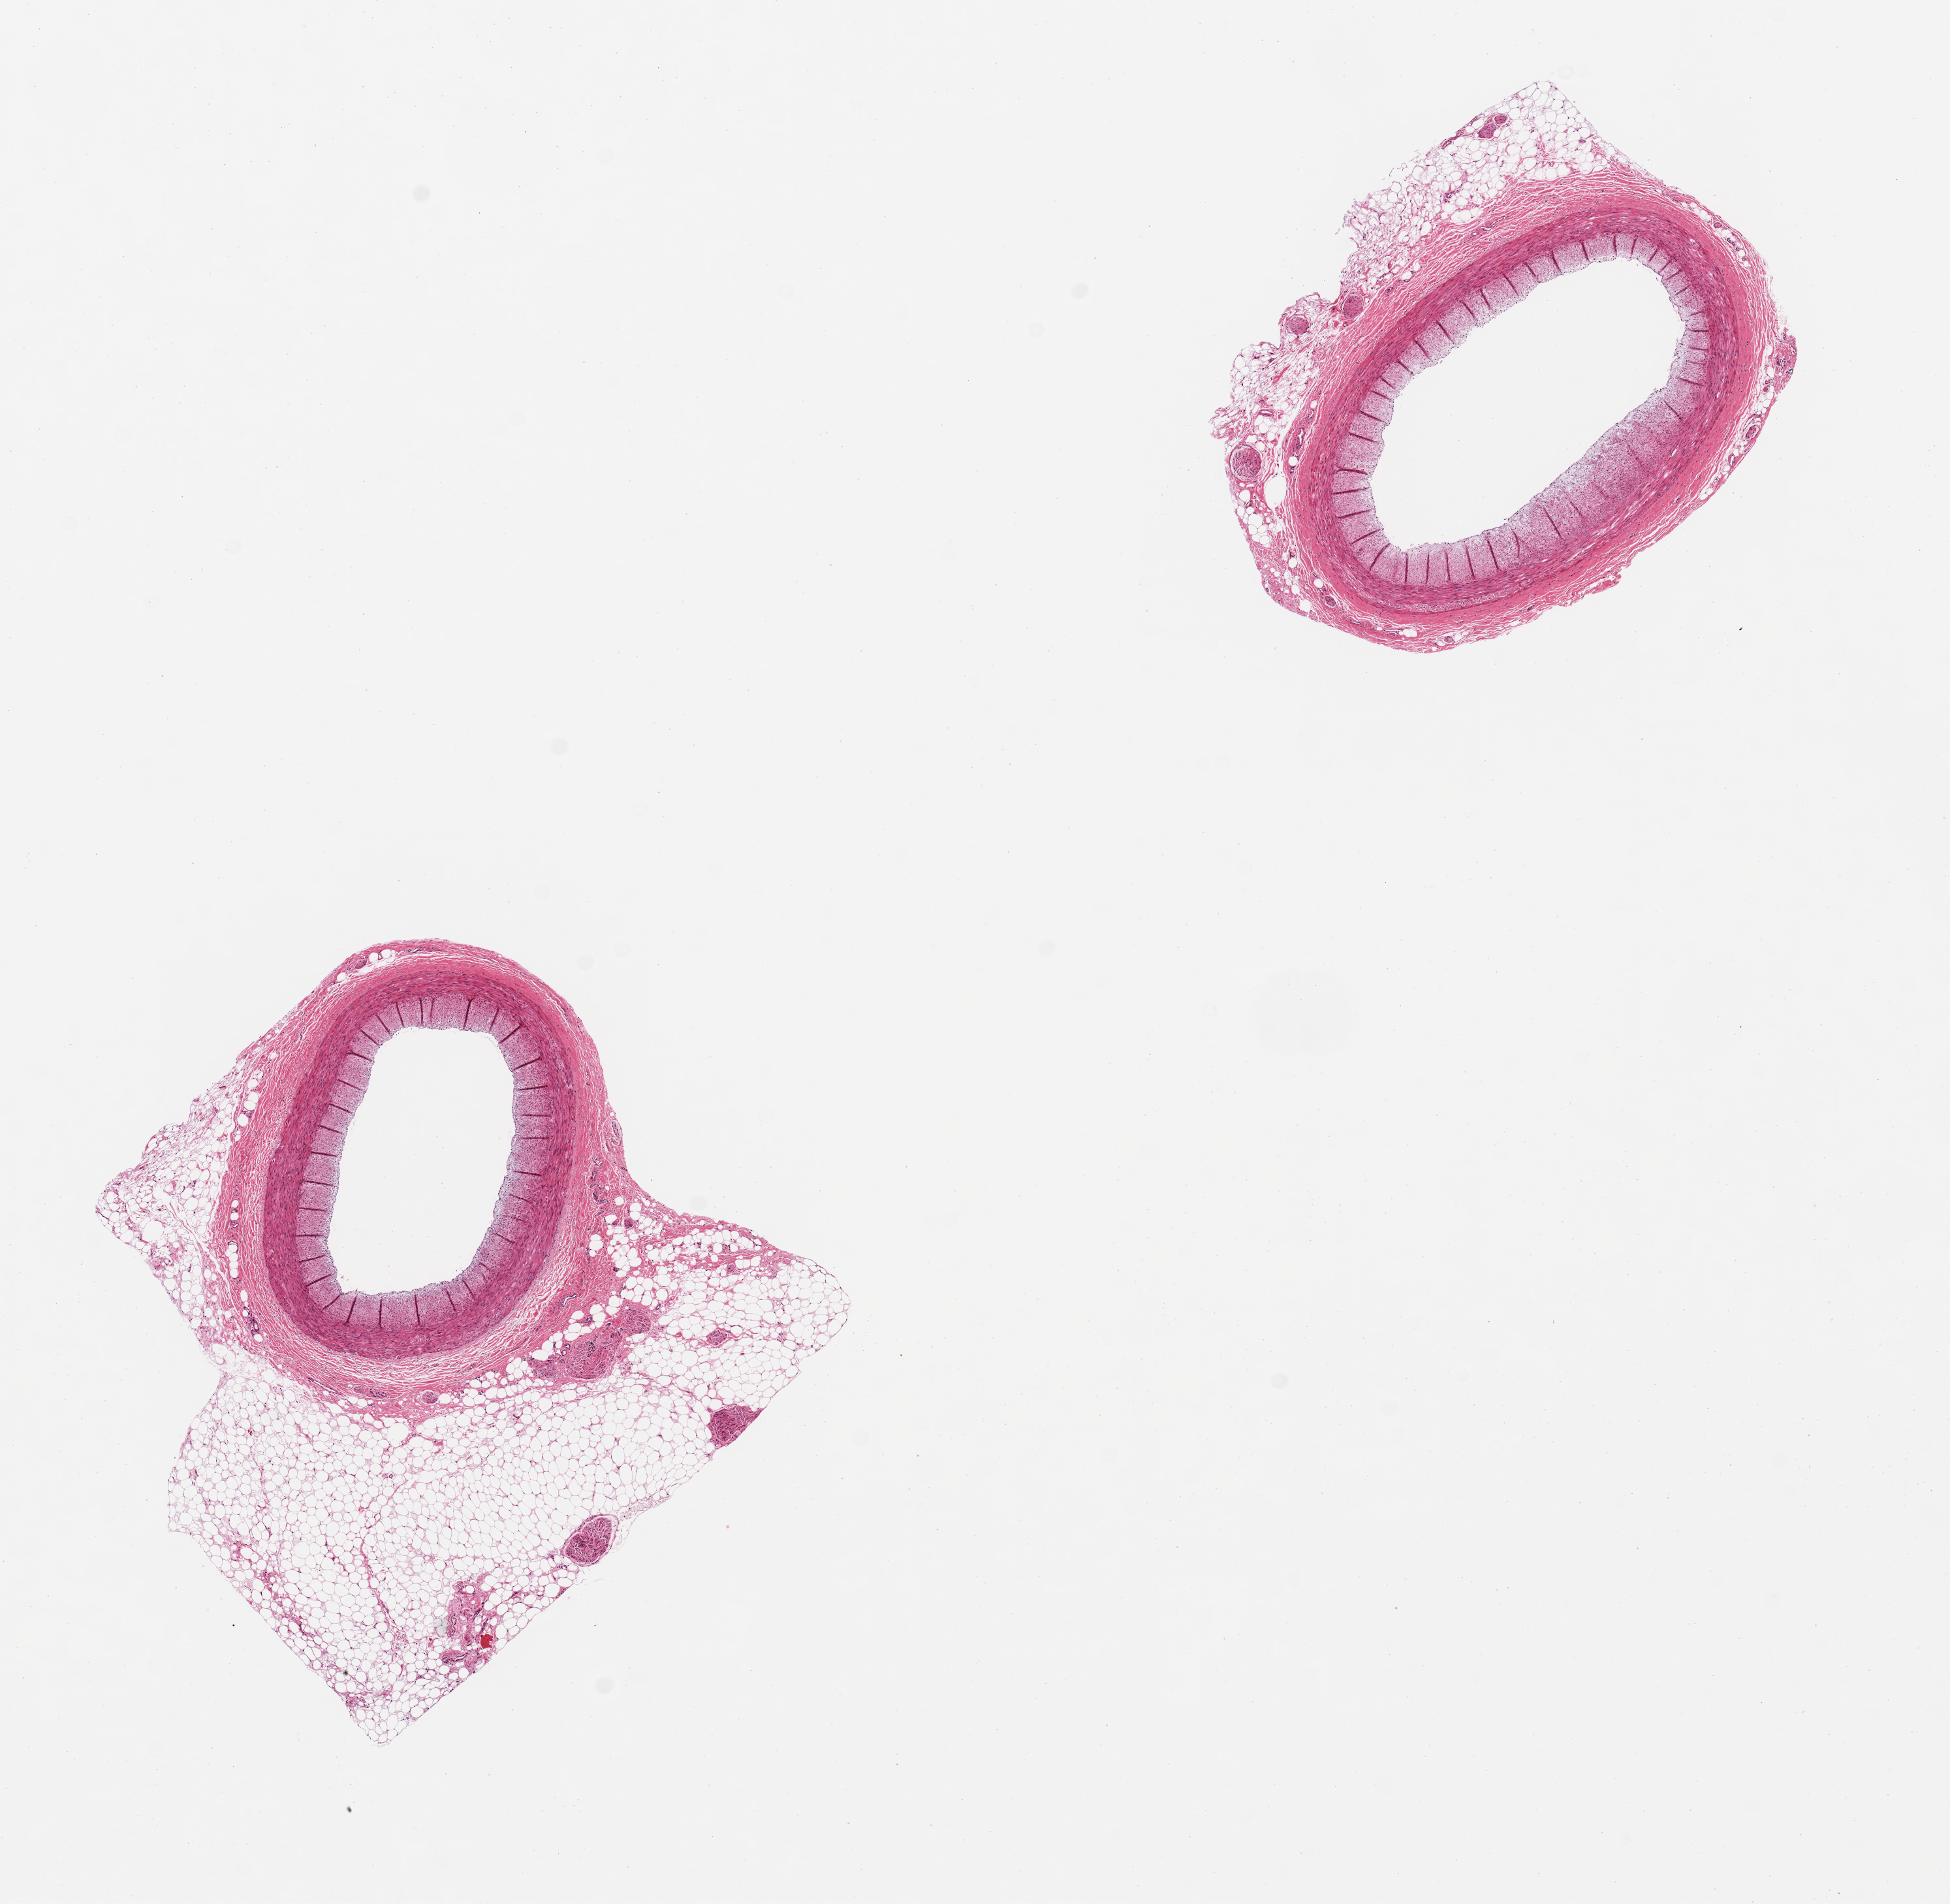
Whole-slide image, hematoxylin and eosin (H&E) stain — low-resolution overview of the scanned area, about 11.8 x 11.5 mm. PAXgene-fixed paraffin-embedded (PFPE) section. Section of coronary artery (target tissue). Tissue donor sample. Donor sex: female.
Pathologist's review note for this sample: 2 pieces; no plaques; widely patent; perivascular fat up to 1.8mm thick.